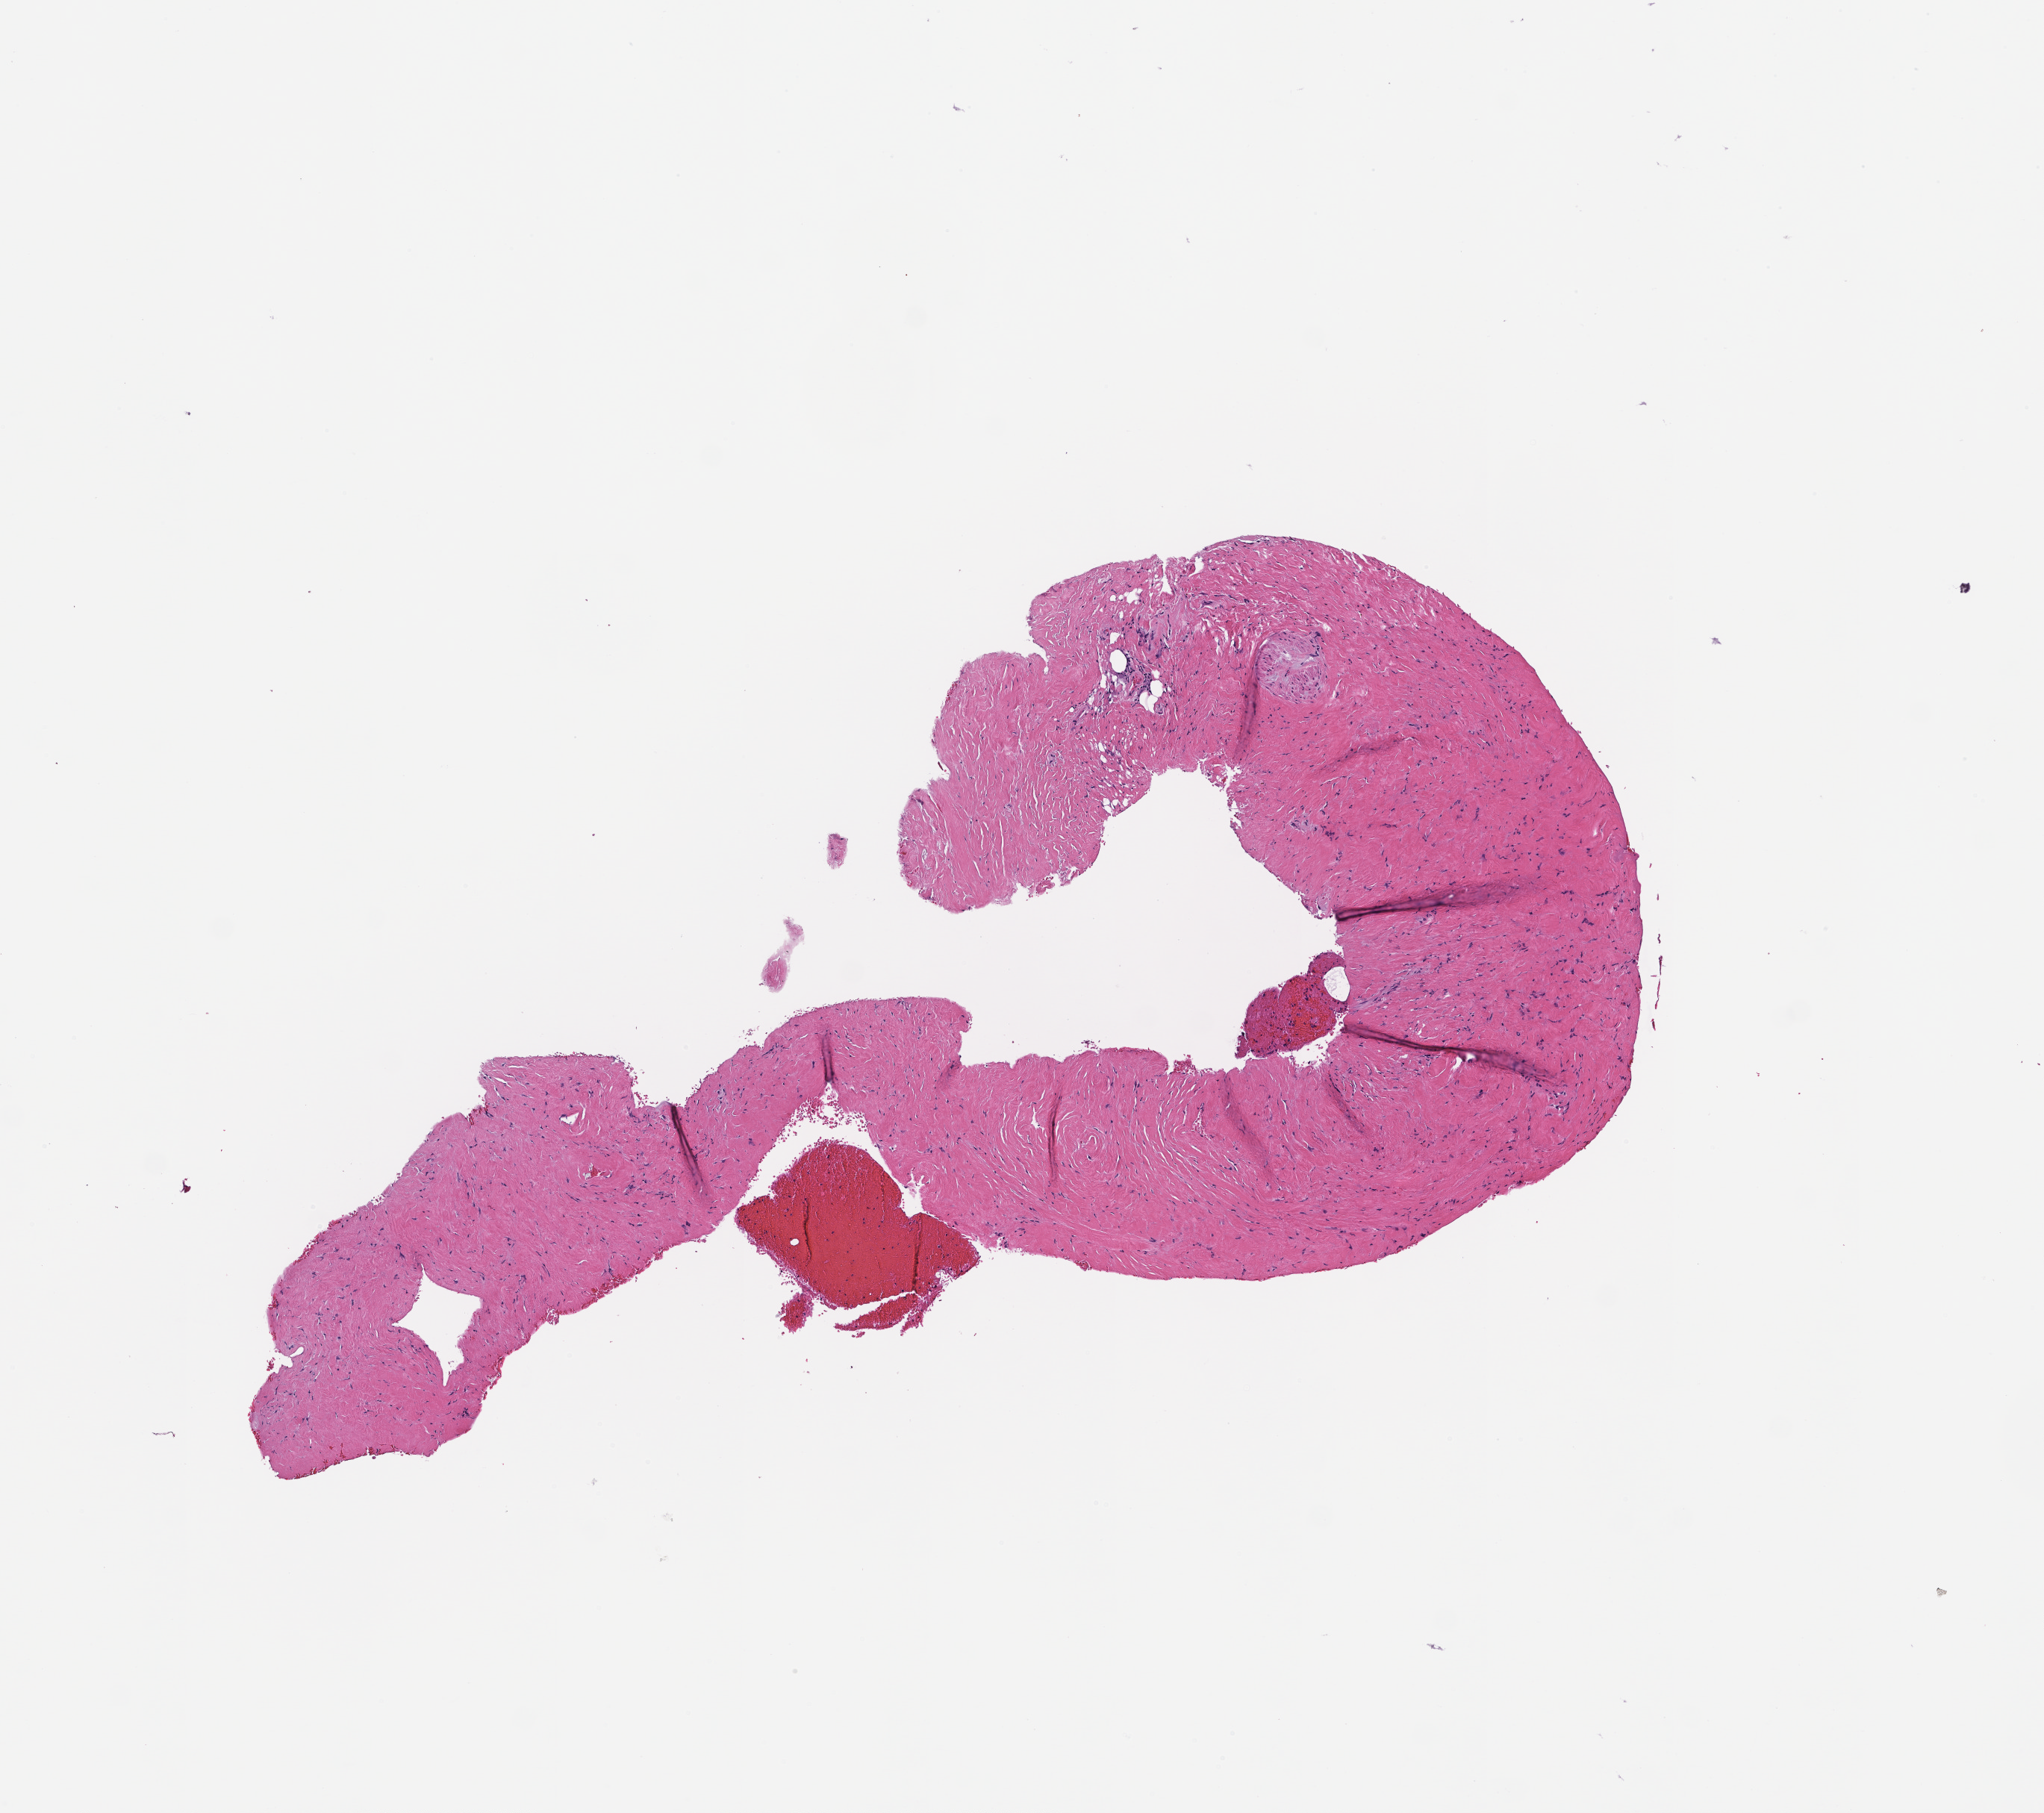
Whole-slide image, hematoxylin and eosin (H&E) stain, a low-resolution overview of the entire scanned area, about 5.5 x 4.9 mm; FFPE section; collected at disease progression. Patient sex: female.
- this section: metastasis (sampled organ not recorded)
- patient diagnosis (primary): Non-Small Cell Lung Carcinoma